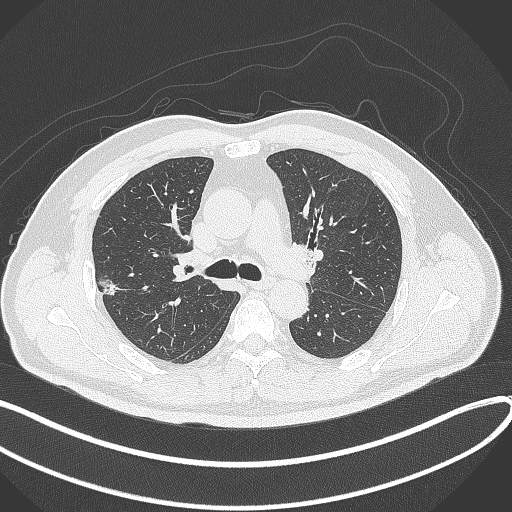
Chest CT, one axial slice; slice 220 of 372 in the series (ordered by position); reconstruction kernel B70f; lung window (W 1500 / L -600 HU); 512 × 512 image matrix. Patient: male, 60 years. From the clinical record (not read from this slice): clinical TNM (as recorded): T1c N0 M0.
Outlined on this slice (bounding box drawn by a radiologist):
- lung tumour (recorded histology: adenocarcinoma): bounding box [x1, y1, x2, y2] px = [94, 271, 123, 300]